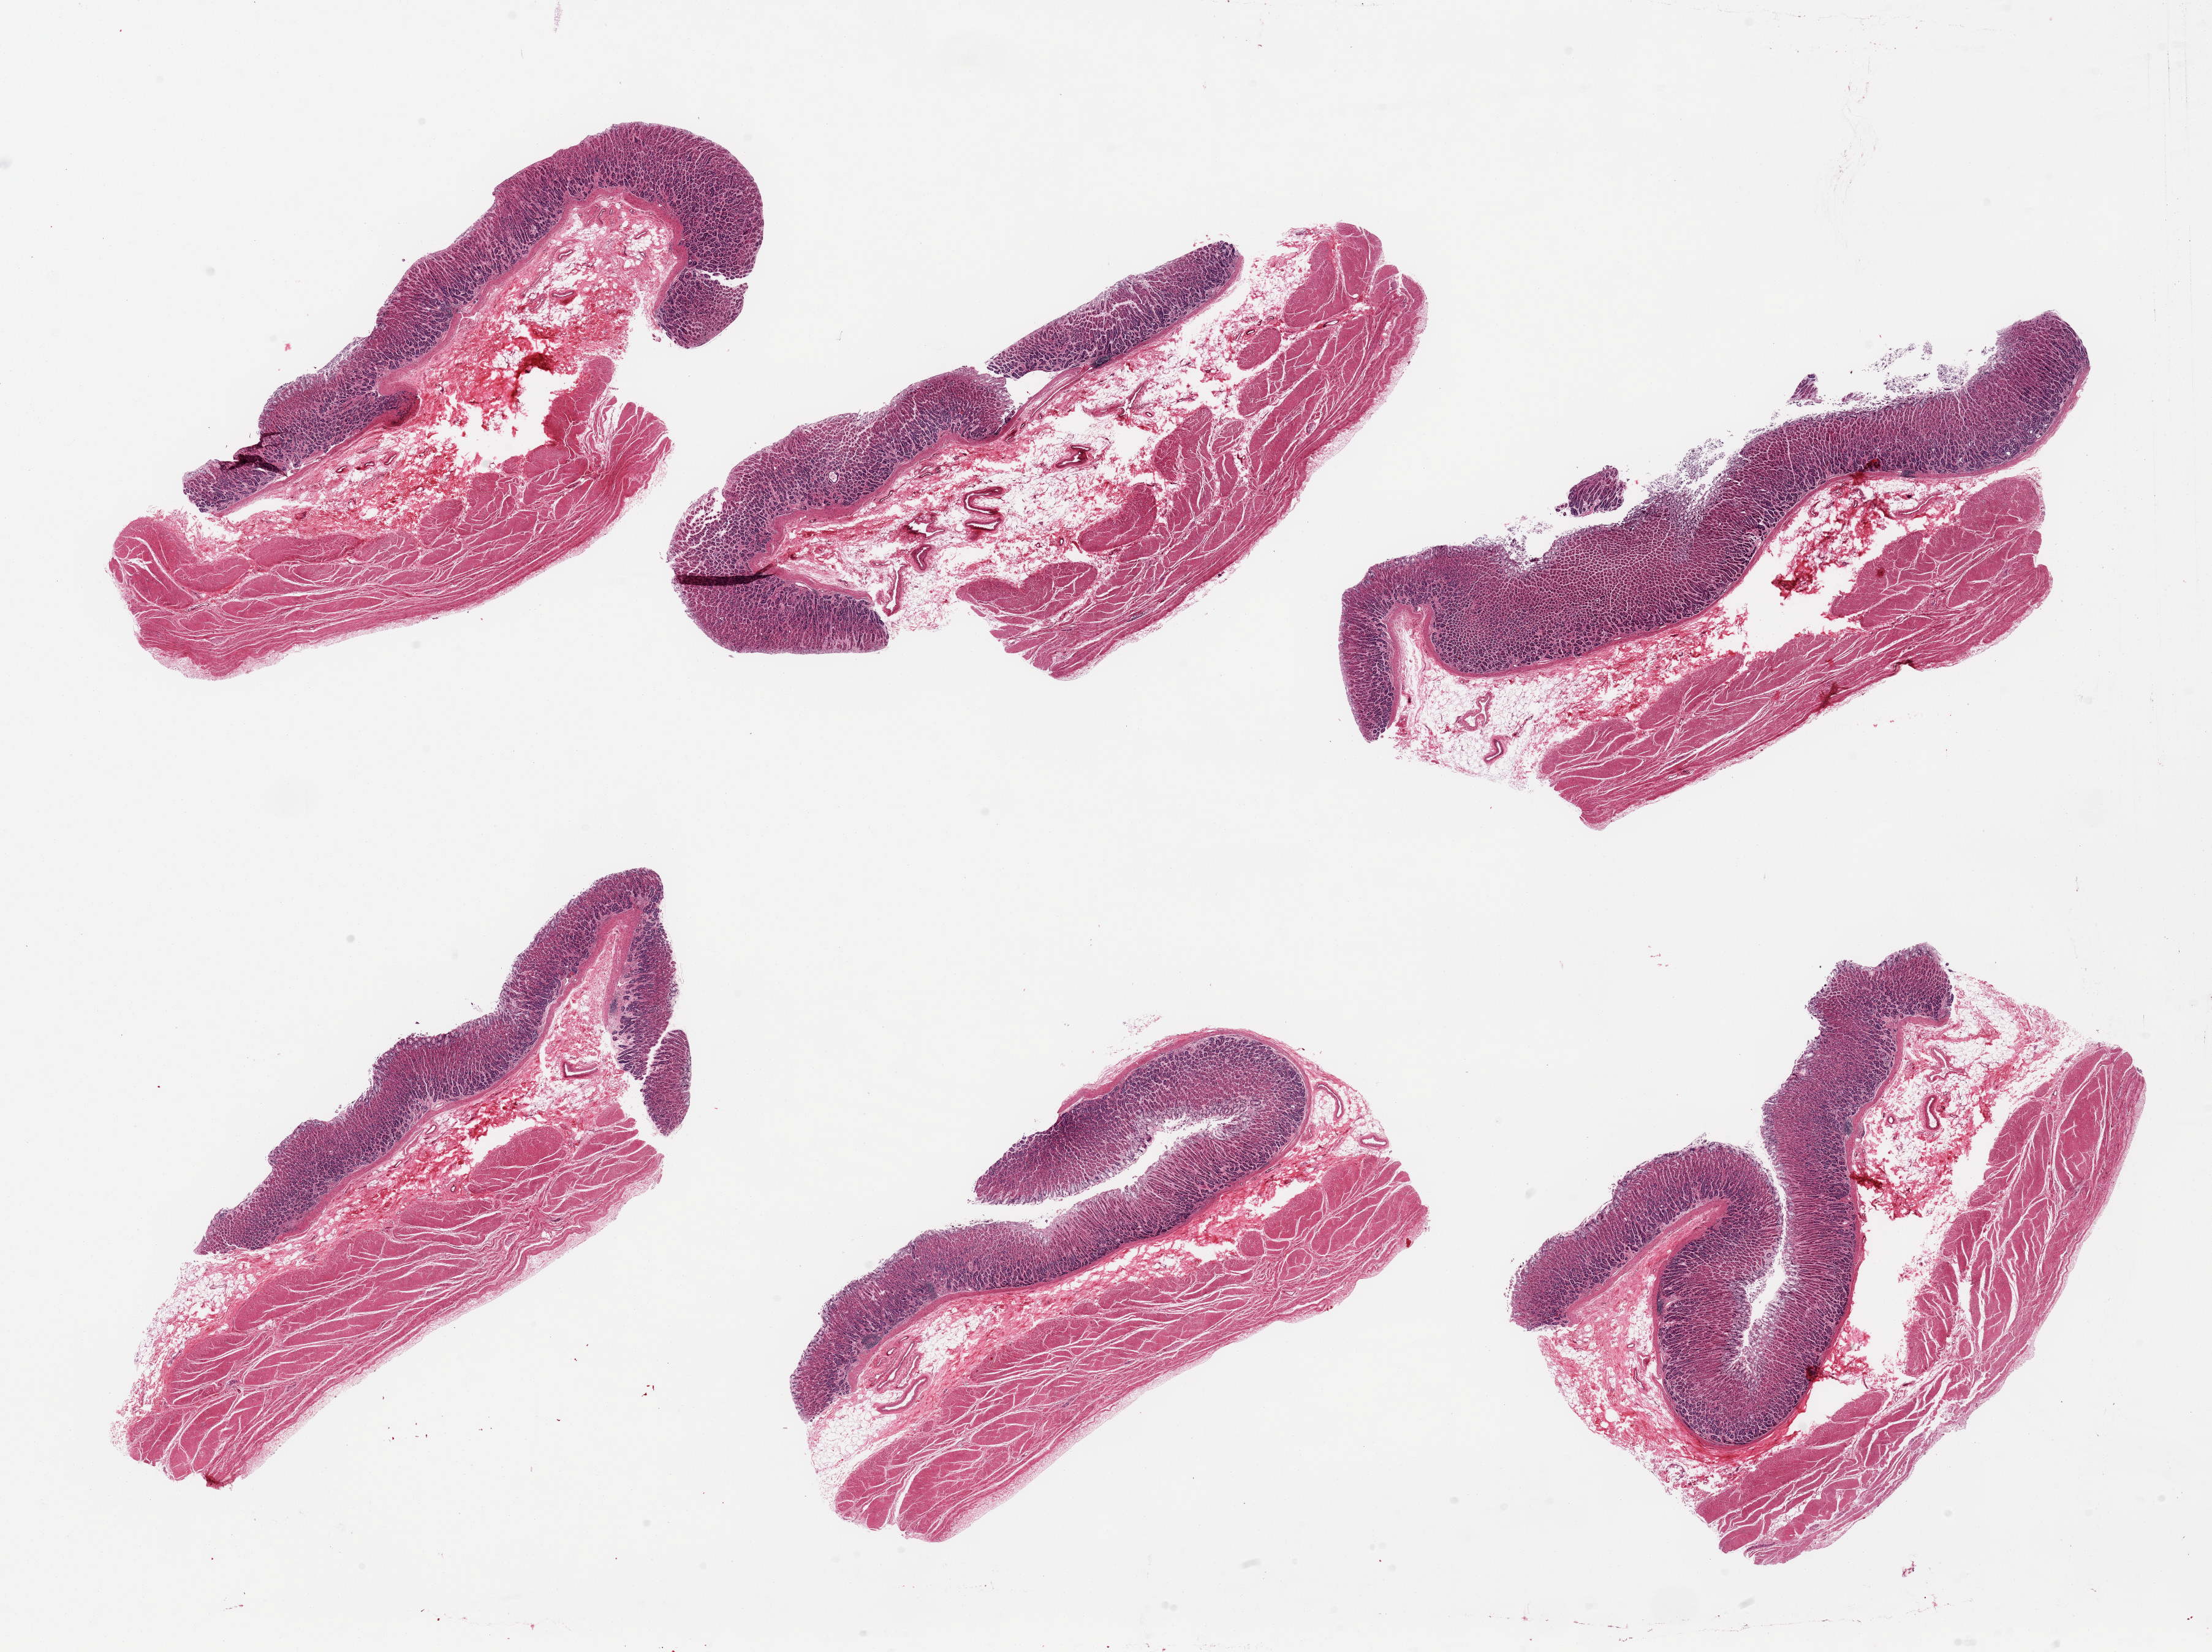
Whole-slide image, haematoxylin and eosin stain — shown as a low-resolution overview of the whole scanned area (about 28.5 x 21.3 mm, from a 20x scan), PAXgene-fixed, paraffin-embedded tissue, sampled site (target tissue): stomach, tissue donor sample.
Pathologist's review note for this sample: 6 pieces, mucosa up to ~1mm.